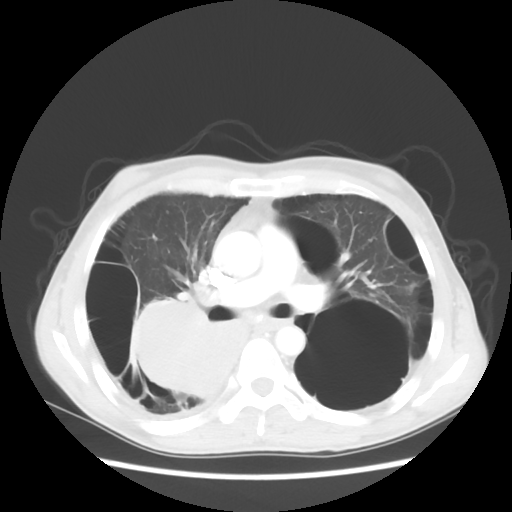
Chest CT, one axial slice; slice 32 of 56 in the series (ordered by position); reconstruction kernel STANDARD; 140 kVp; lung window (W 1500 / L -600 HU); 512 × 512 image matrix, field of view 351 × 351 mm. Male patient, age 41 years. From the clinical record (not read from this slice): clinical TNM (as recorded): T4 N0 M1a.
Outlined on this slice (rectangle marked by the reading radiologist):
- lung tumour (recorded histology: large cell carcinoma): bounding box [x1, y1, x2, y2] px = [120, 291, 253, 410]